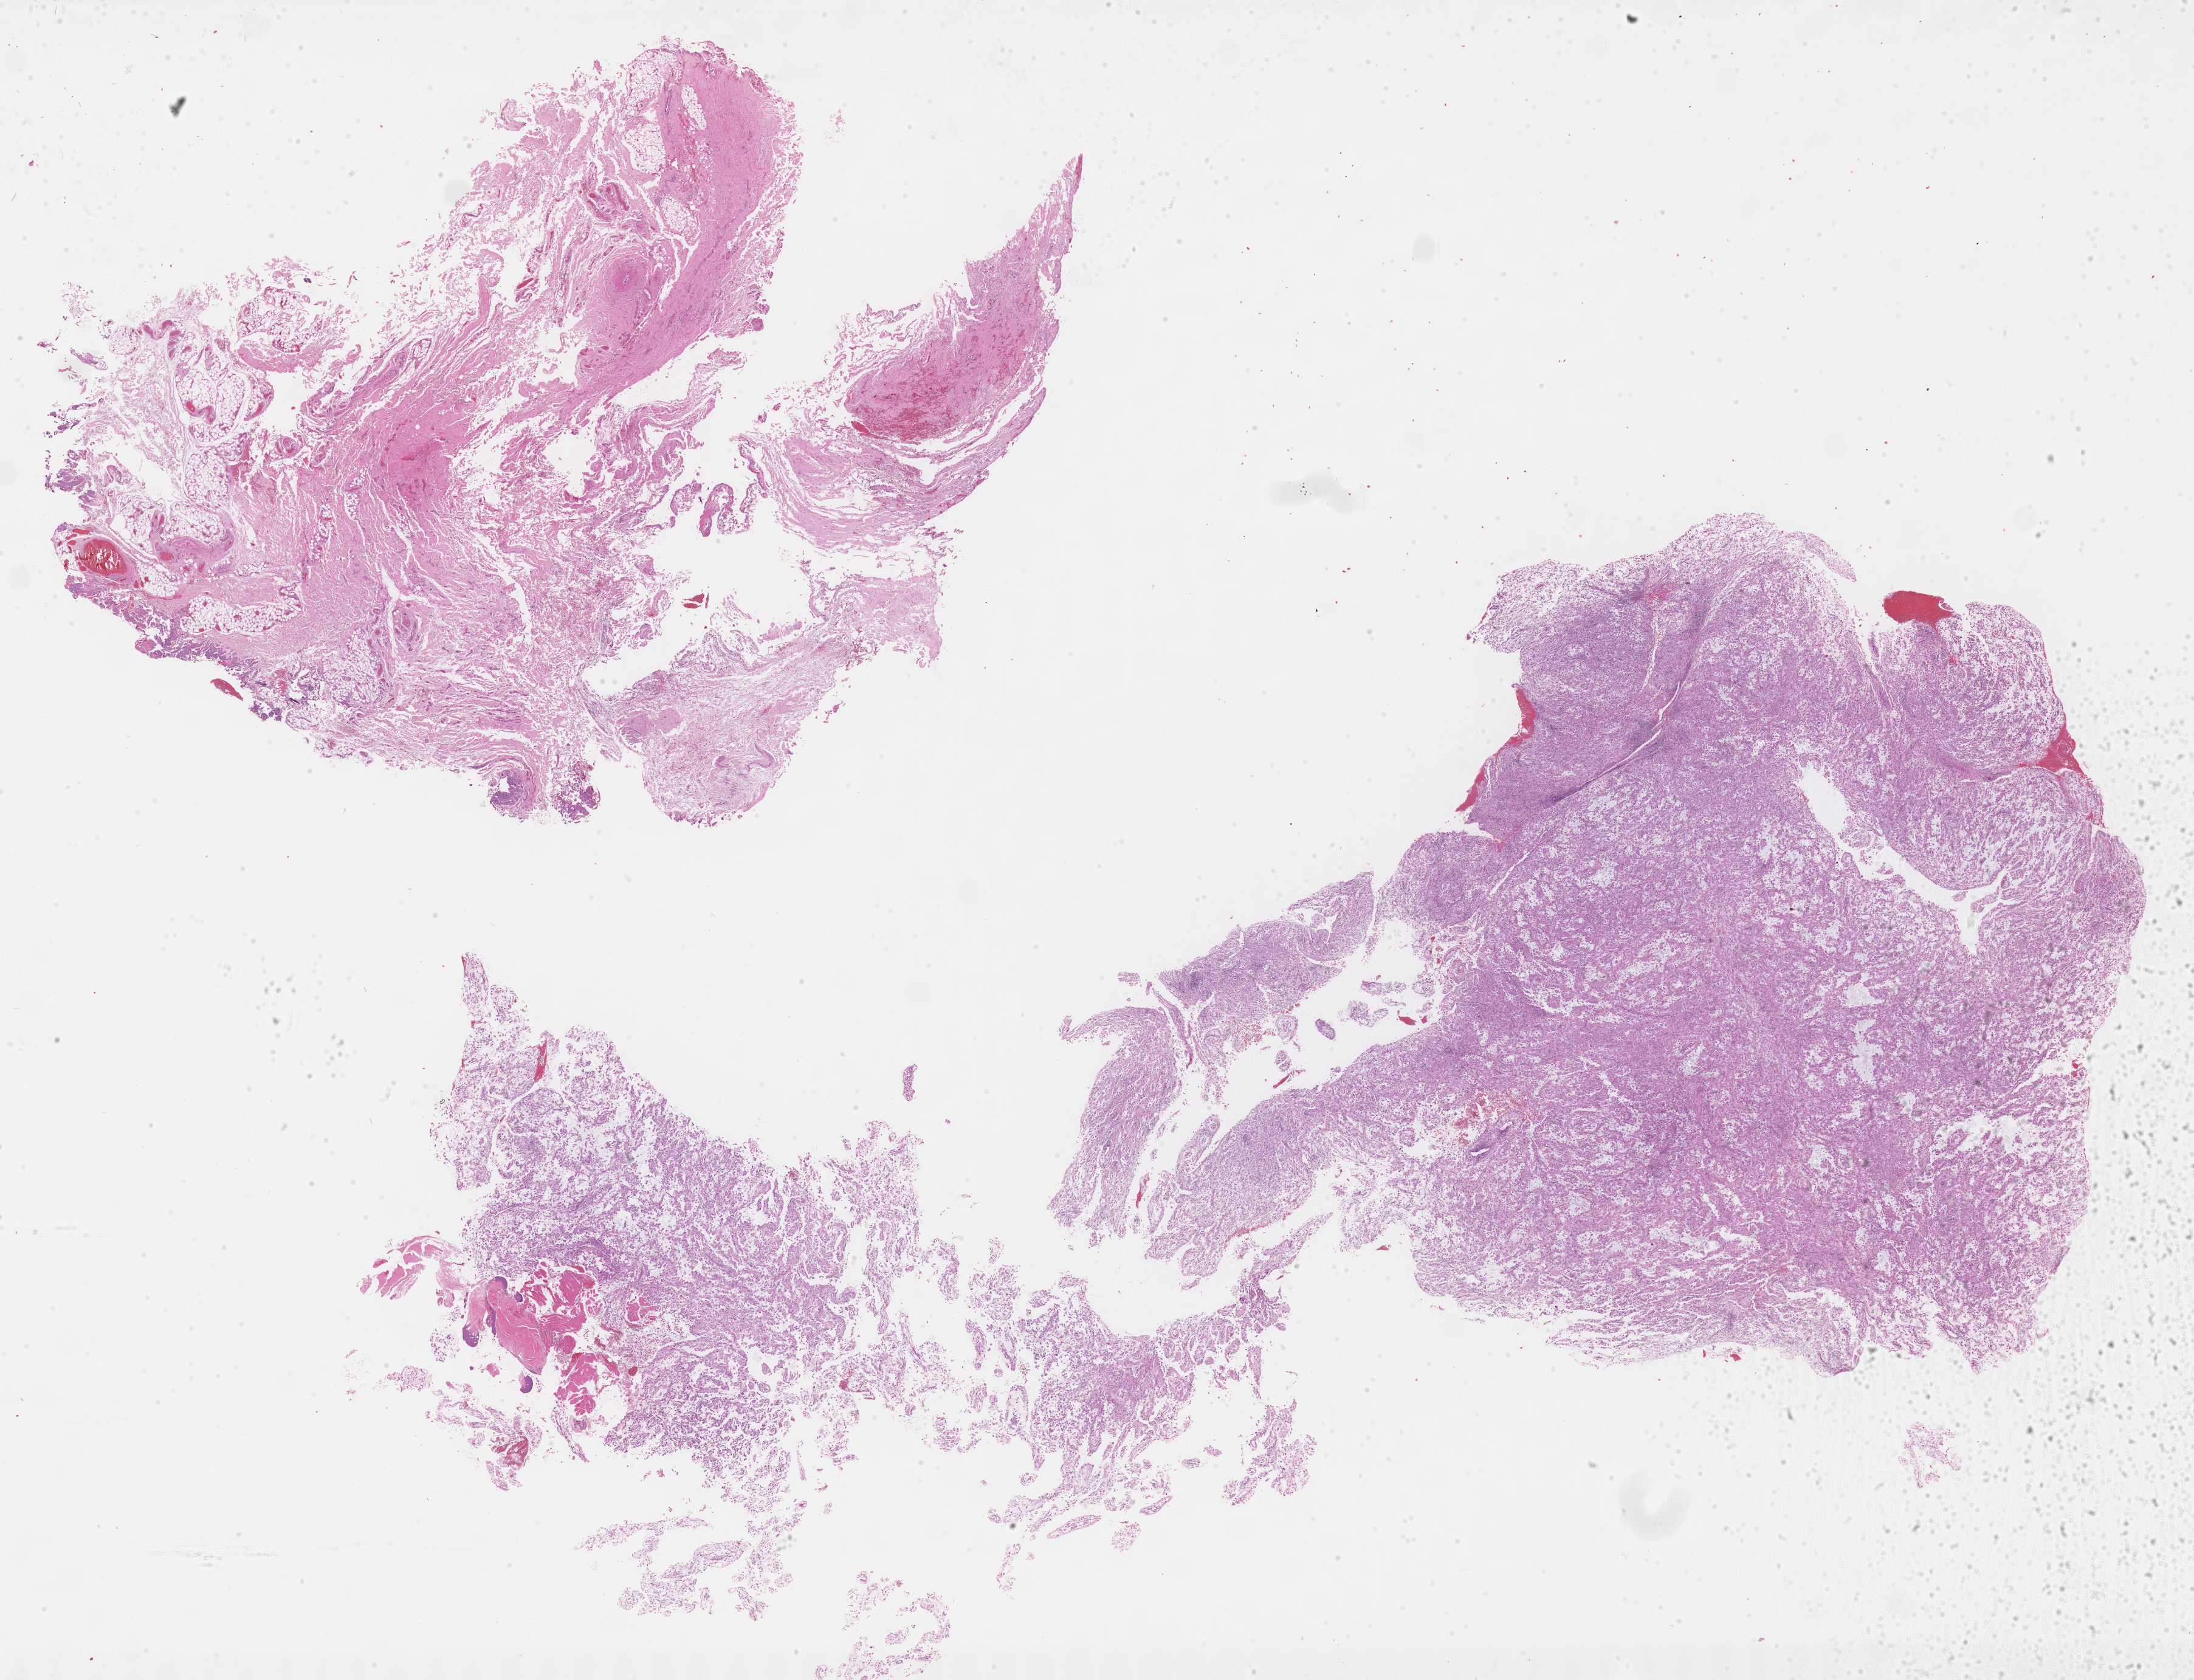
Haematoxylin and eosin whole-slide image of tumor tissue, shown as a low-resolution overview of the whole scanned area (about 29.2 x 22.3 mm); formalin-fixed, paraffin-embedded (FFPE) tissue; sample anatomic site: neck, posterior. Male patient, age at diagnosis 6.5 years.
- stage (as recorded): 3
- diagnosis: rhabdomyosarcoma; histological classification: embryonal rhabdomyosarcoma
- metastatic status at presentation (as recorded): non-metastatic